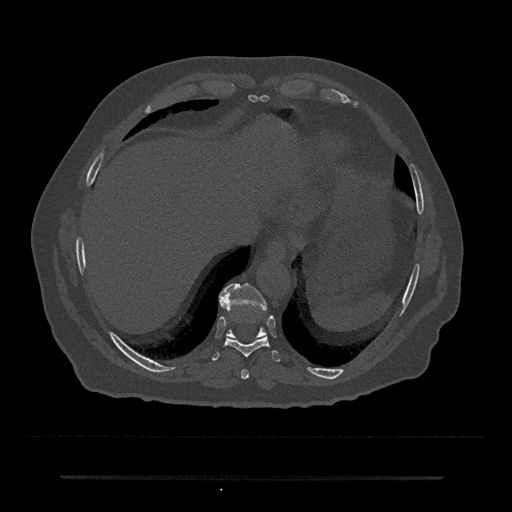
CT including the spine, one axial slice; slice 266 of 797 in the series (ordered by position); bone window (W 1800 / L 400 HU); 0.5 mm slice thickness; 512 × 512 image matrix, field of view 437 × 437 mm. Patient: male, 69 years. Case-level facts recorded for this patient, not image findings: primary cancer: prostate.
Outlined on this slice (semi-automatic segmentation, software-assisted and operator-edited):
- T10 vertebra: box from (x=219, y=283) to (x=267, y=339) px
- T8 vertebra: (x=241, y=369)–(x=249, y=379)
- T9 vertebra: (x=211, y=291)–(x=281, y=362)